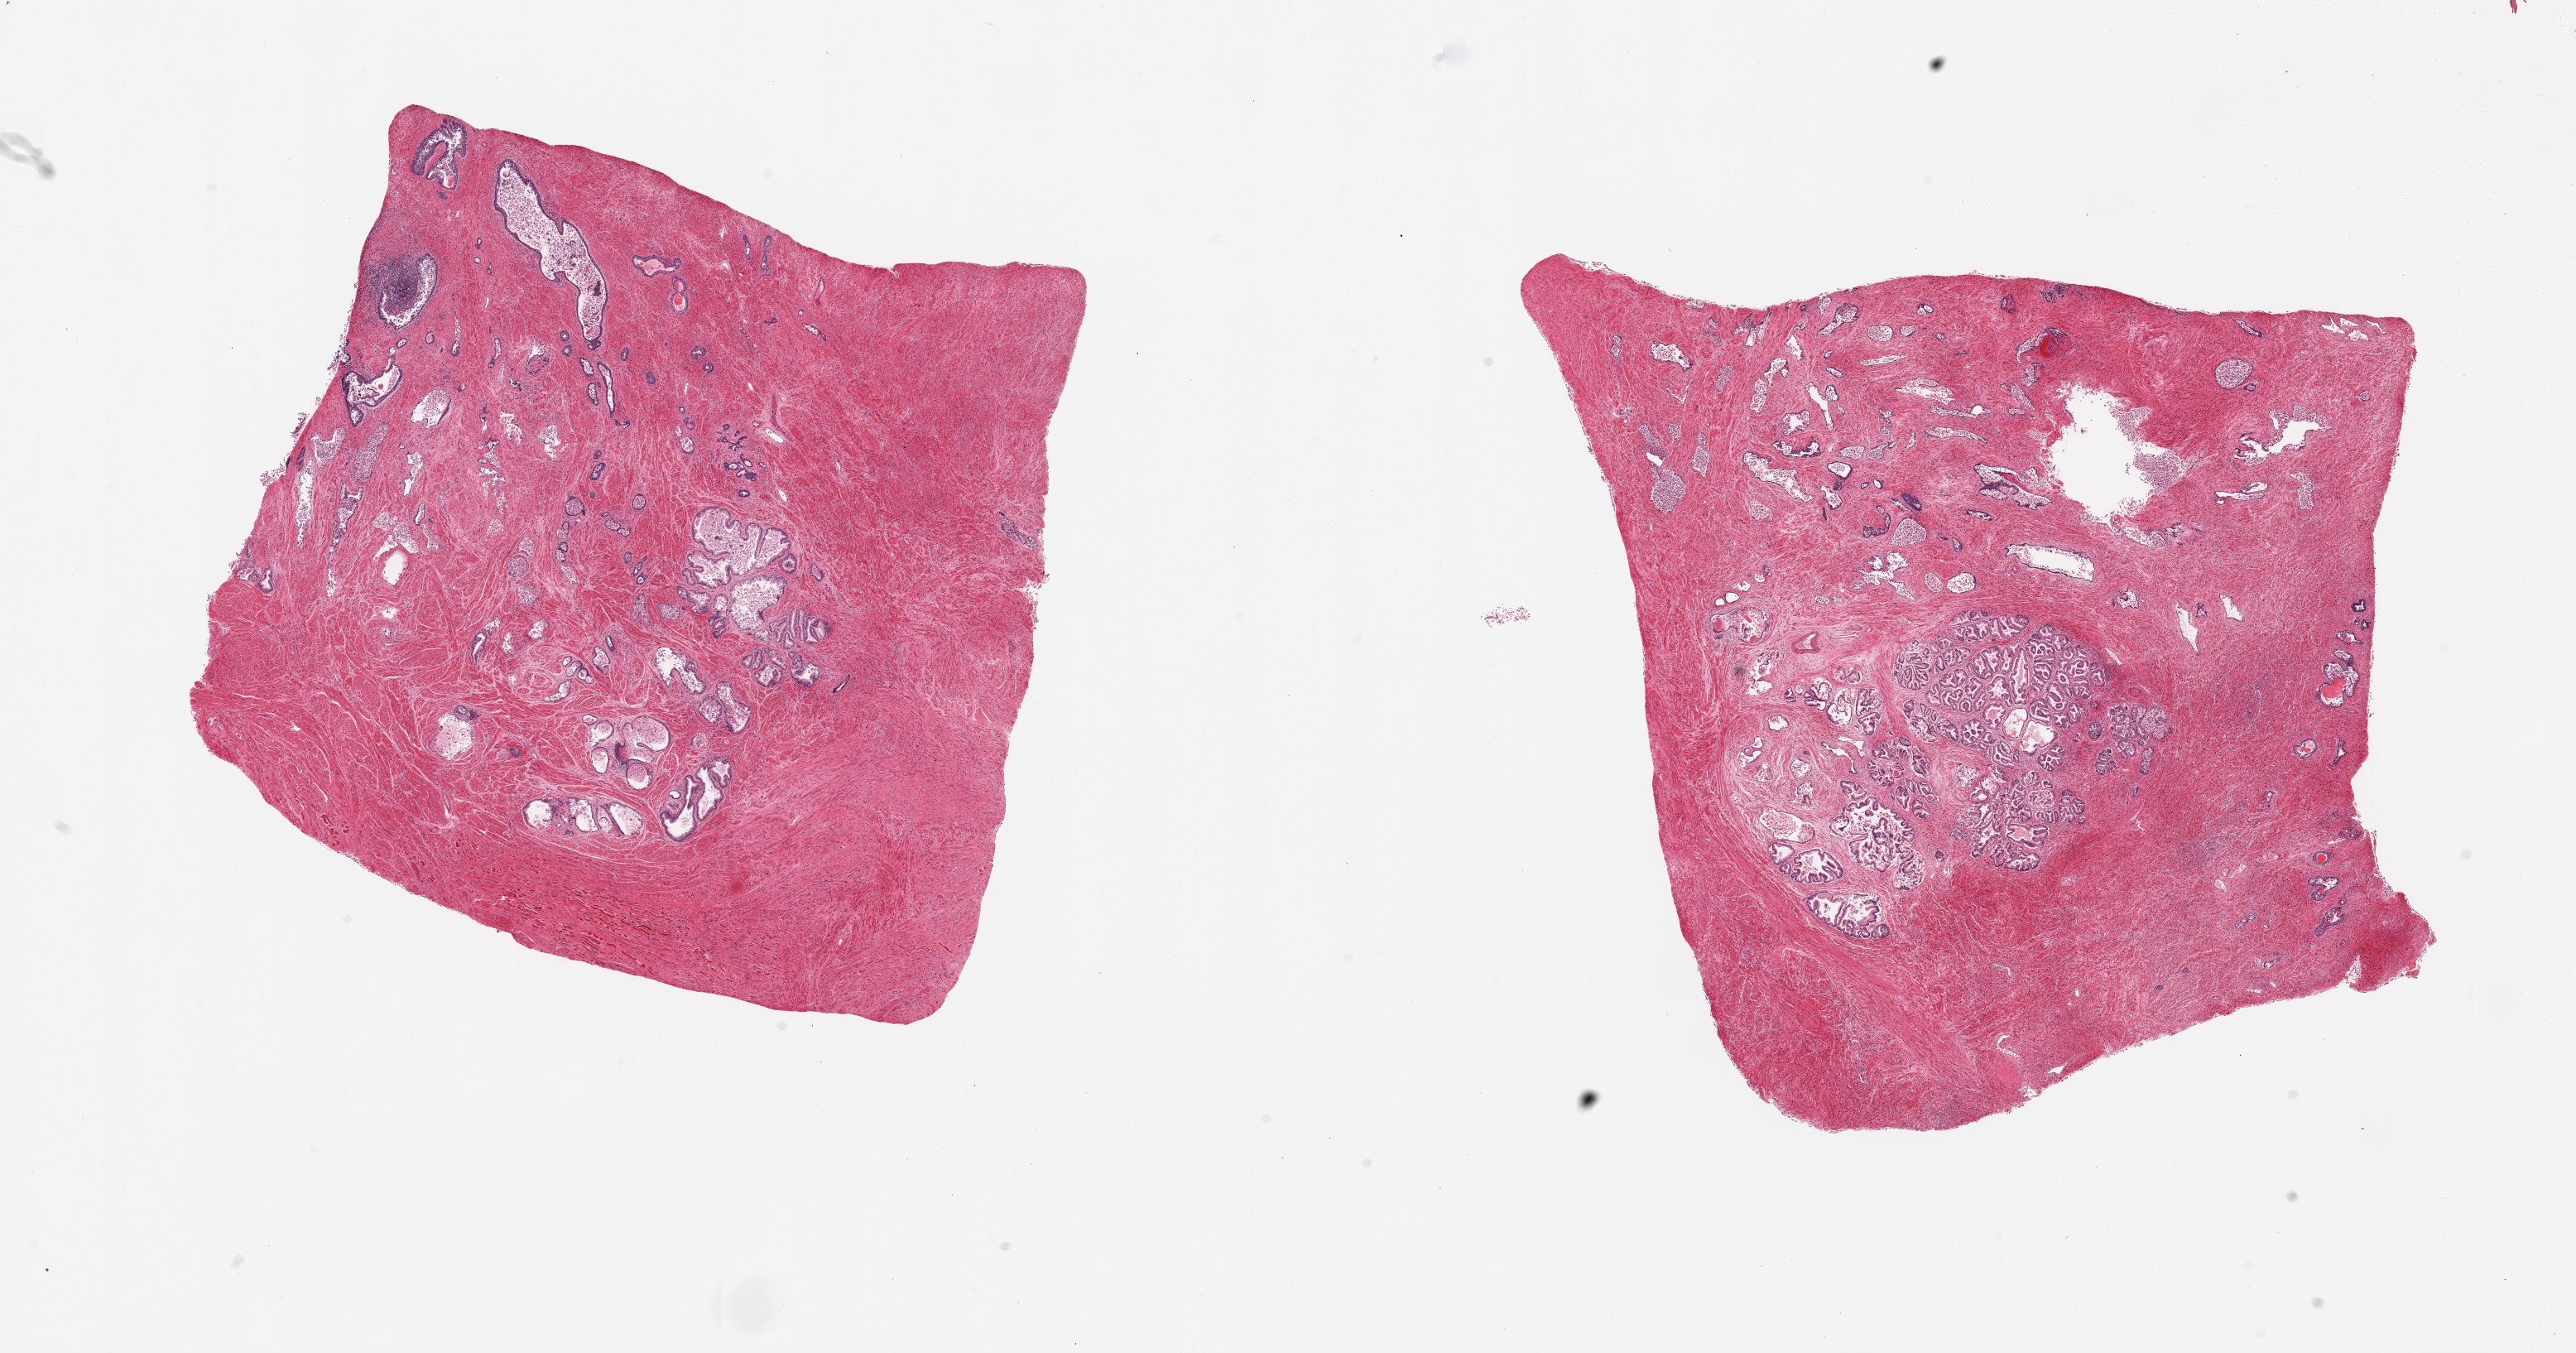
Whole-slide image, haematoxylin and eosin stain, brightfield, a low-resolution overview of the entire scanned area, about 24.6 x 12.9 mm (from a 20x scan); PAXgene-fixed, paraffin-embedded tissue; sampled site (target tissue): prostate; tissue donor sample. Donor: male.
Pathologist's review note for this sample: 2 pieces, hyperplastic glandular pattern, focal chronic prostatitis.